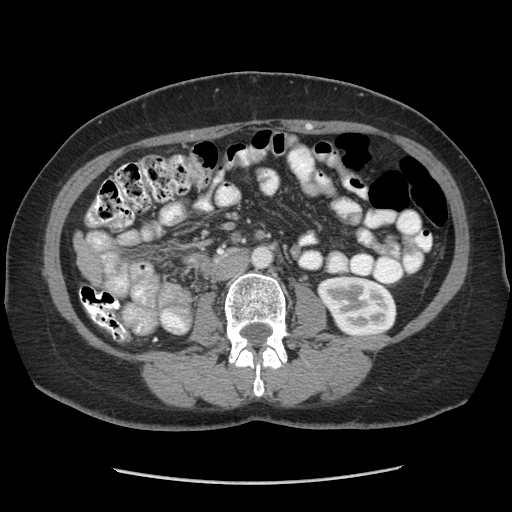
Contrast-enhanced abdominal CT (liver protocol), one axial slice. Position 109 of 185 along the scan axis. 140 kVp. Soft-tissue window (W 400 / L 40 HU). 2.5 mm slice thickness. 512 × 512 image matrix. From the clinical record (not read from this slice): diagnosis: hepatocellular carcinoma (patient treated with transarterial chemoembolisation; whether this scan precedes or follows treatment is not stated here); TNM stage (as recorded): Stage-I.
Structures marked on this image (semi-automatic segmentation, software-assisted and operator-edited):
- liver parenchyma outside the tumour (the mass and vessels are separate outlines, so this box may not span the whole liver): bounding box <74,233,100,281> (left, top, right, bottom; pixels)